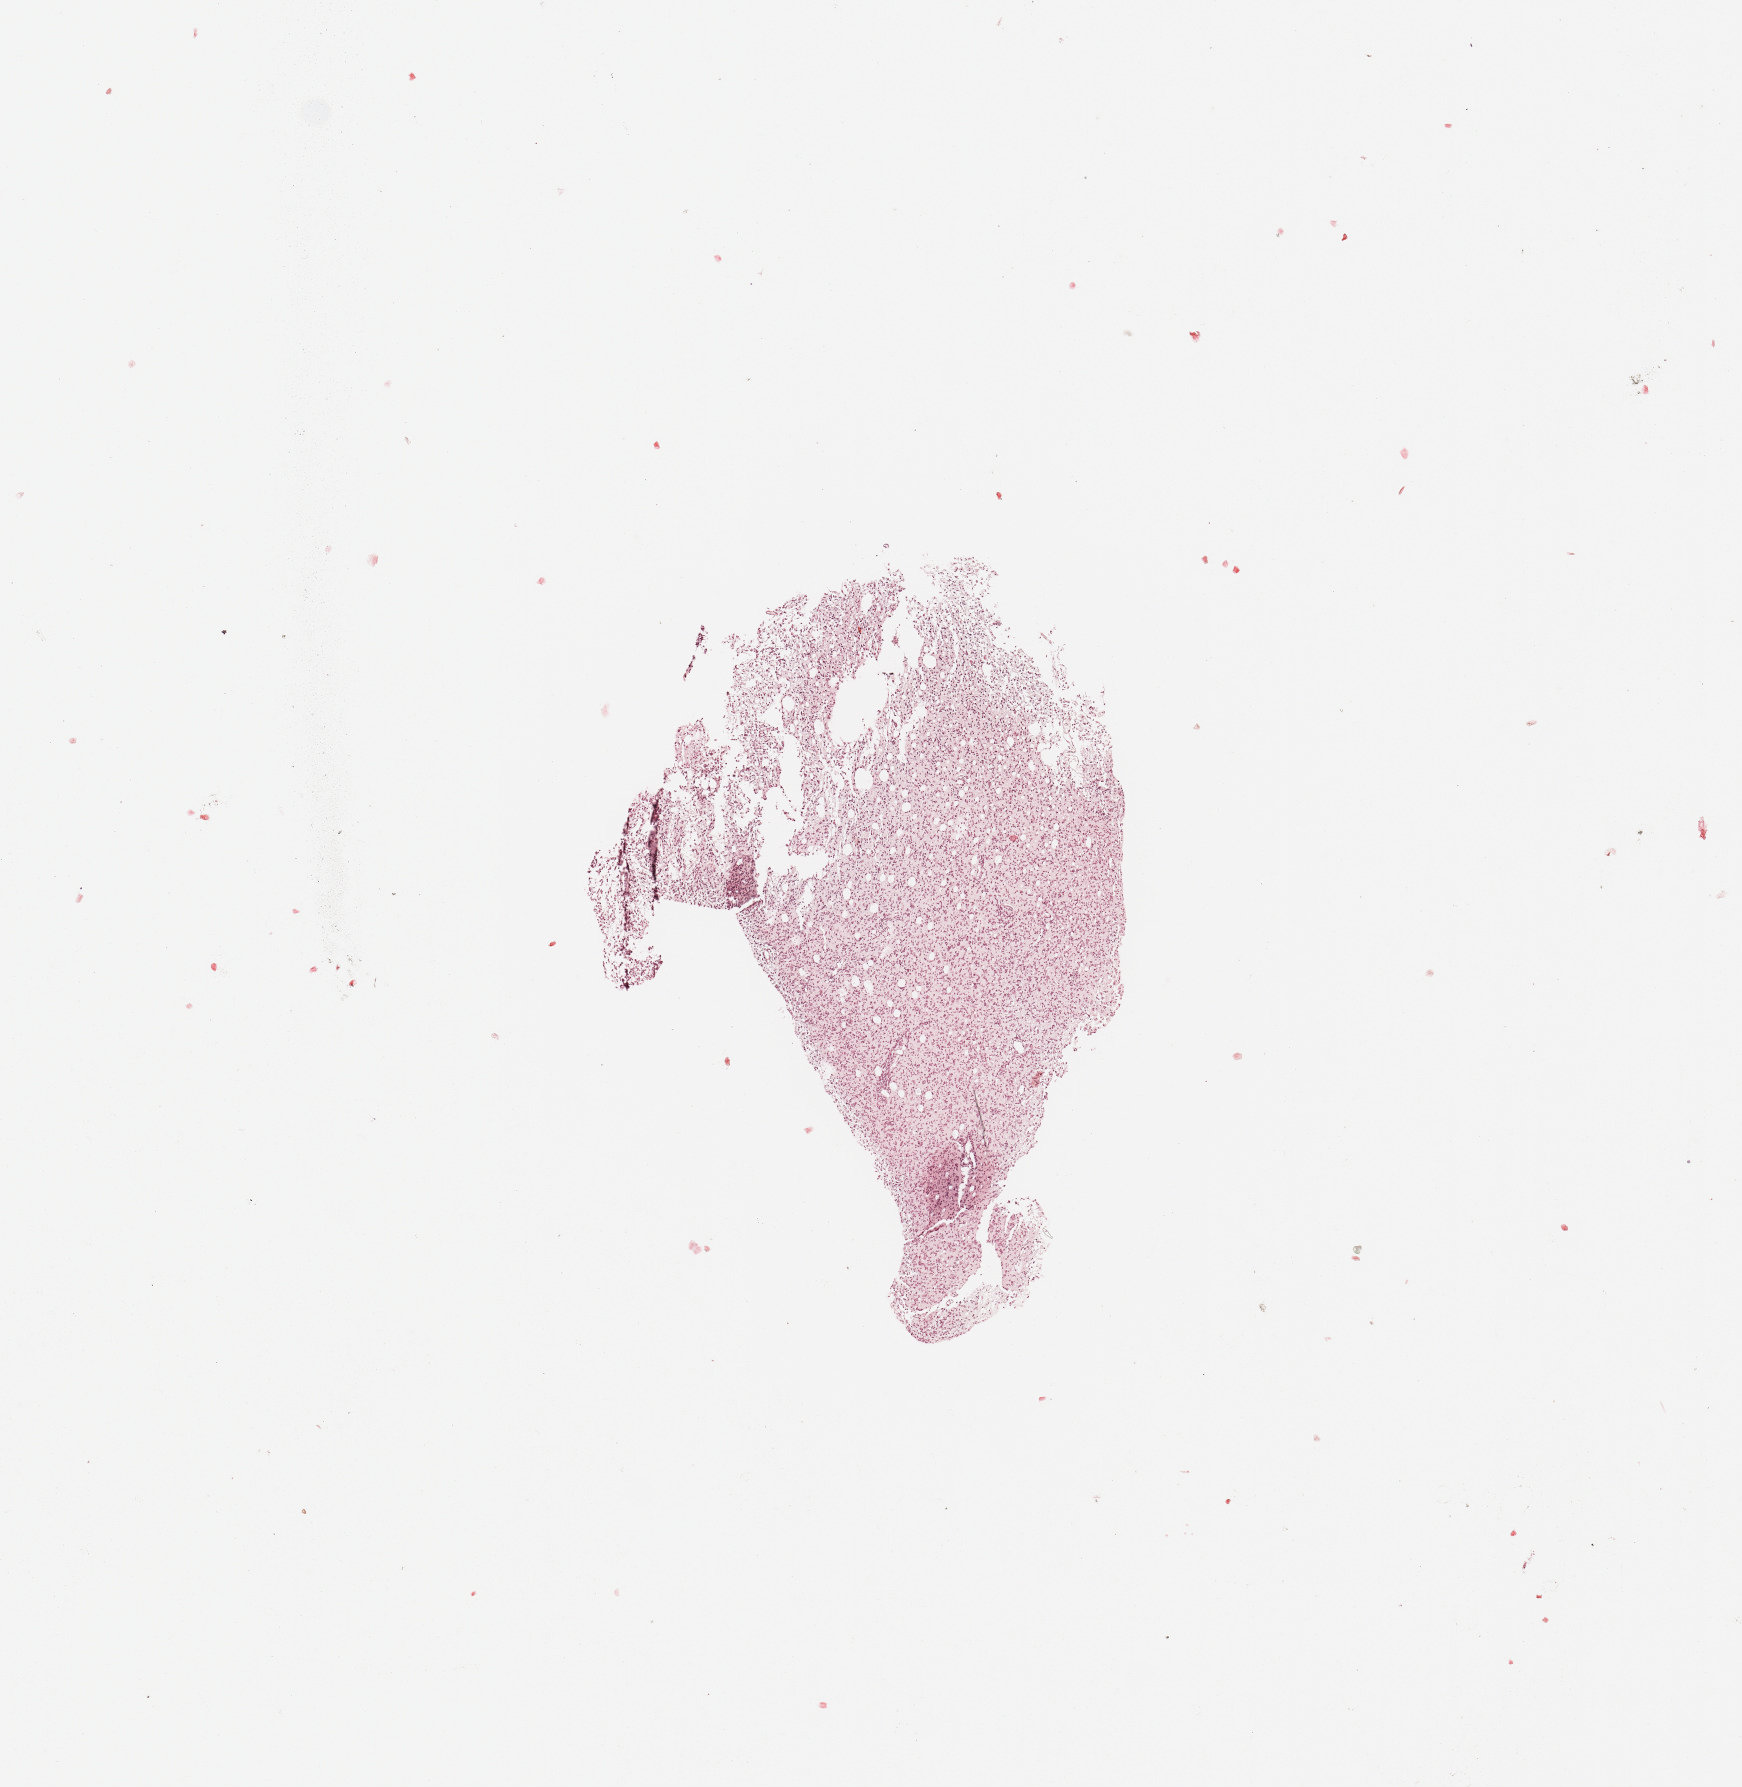
Digitized H&E-stained tissue section (whole slide) — low-resolution overview of the scanned area, about 6.9 x 7.1 mm (slide scanned at 20x), tumour tissue sample, sampled site: brain. Female, 69 y/o. Slide review estimates, as recorded: tumour nuclei 85%, necrosis 2%.
Diagnosis: Glioblastoma.